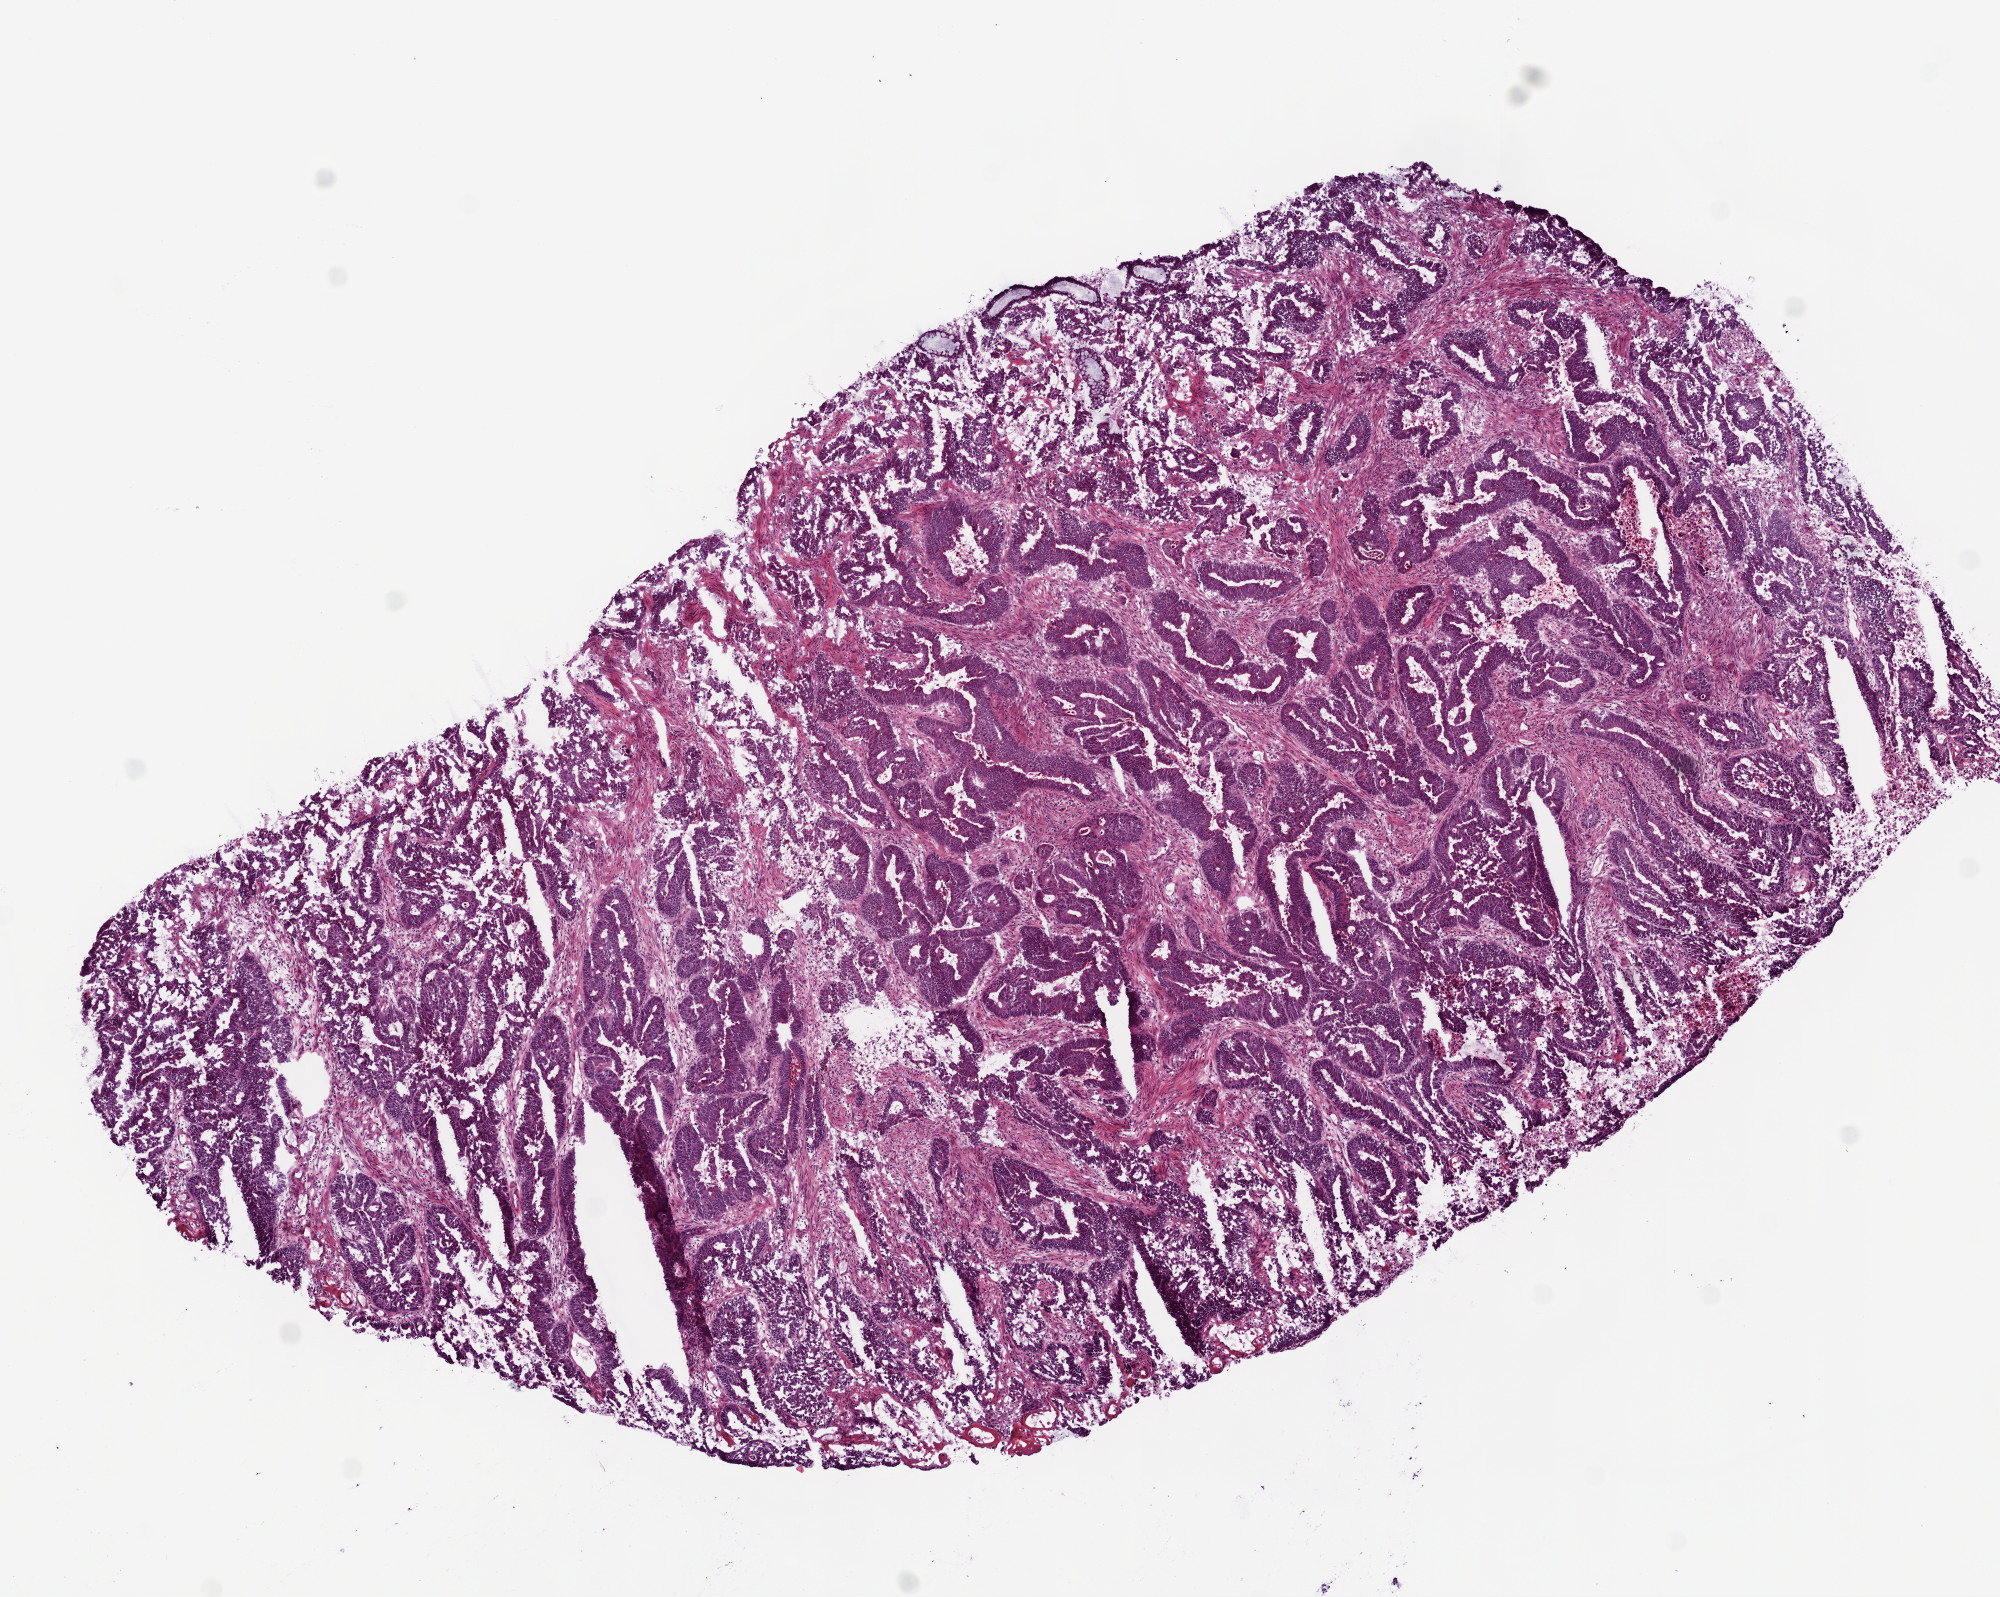
H&E-stained whole-slide image — a low-resolution overview of the entire scanned area, about 8.0 x 6.4 mm, frozen section from the bottom of the tissue portion, primary tumour sample from the colon. Male, age 65 years at initial diagnosis. Slide review estimates, as recorded: tumour cells 99%, tumour nuclei 85%, necrosis 1%. Inflammatory infiltration, as recorded: lymphocyte infiltration 1%.
Pathologic diagnosis: Adenocarcinoma, NOS (descending colon). AJCC pathologic stage: III (5th edition).